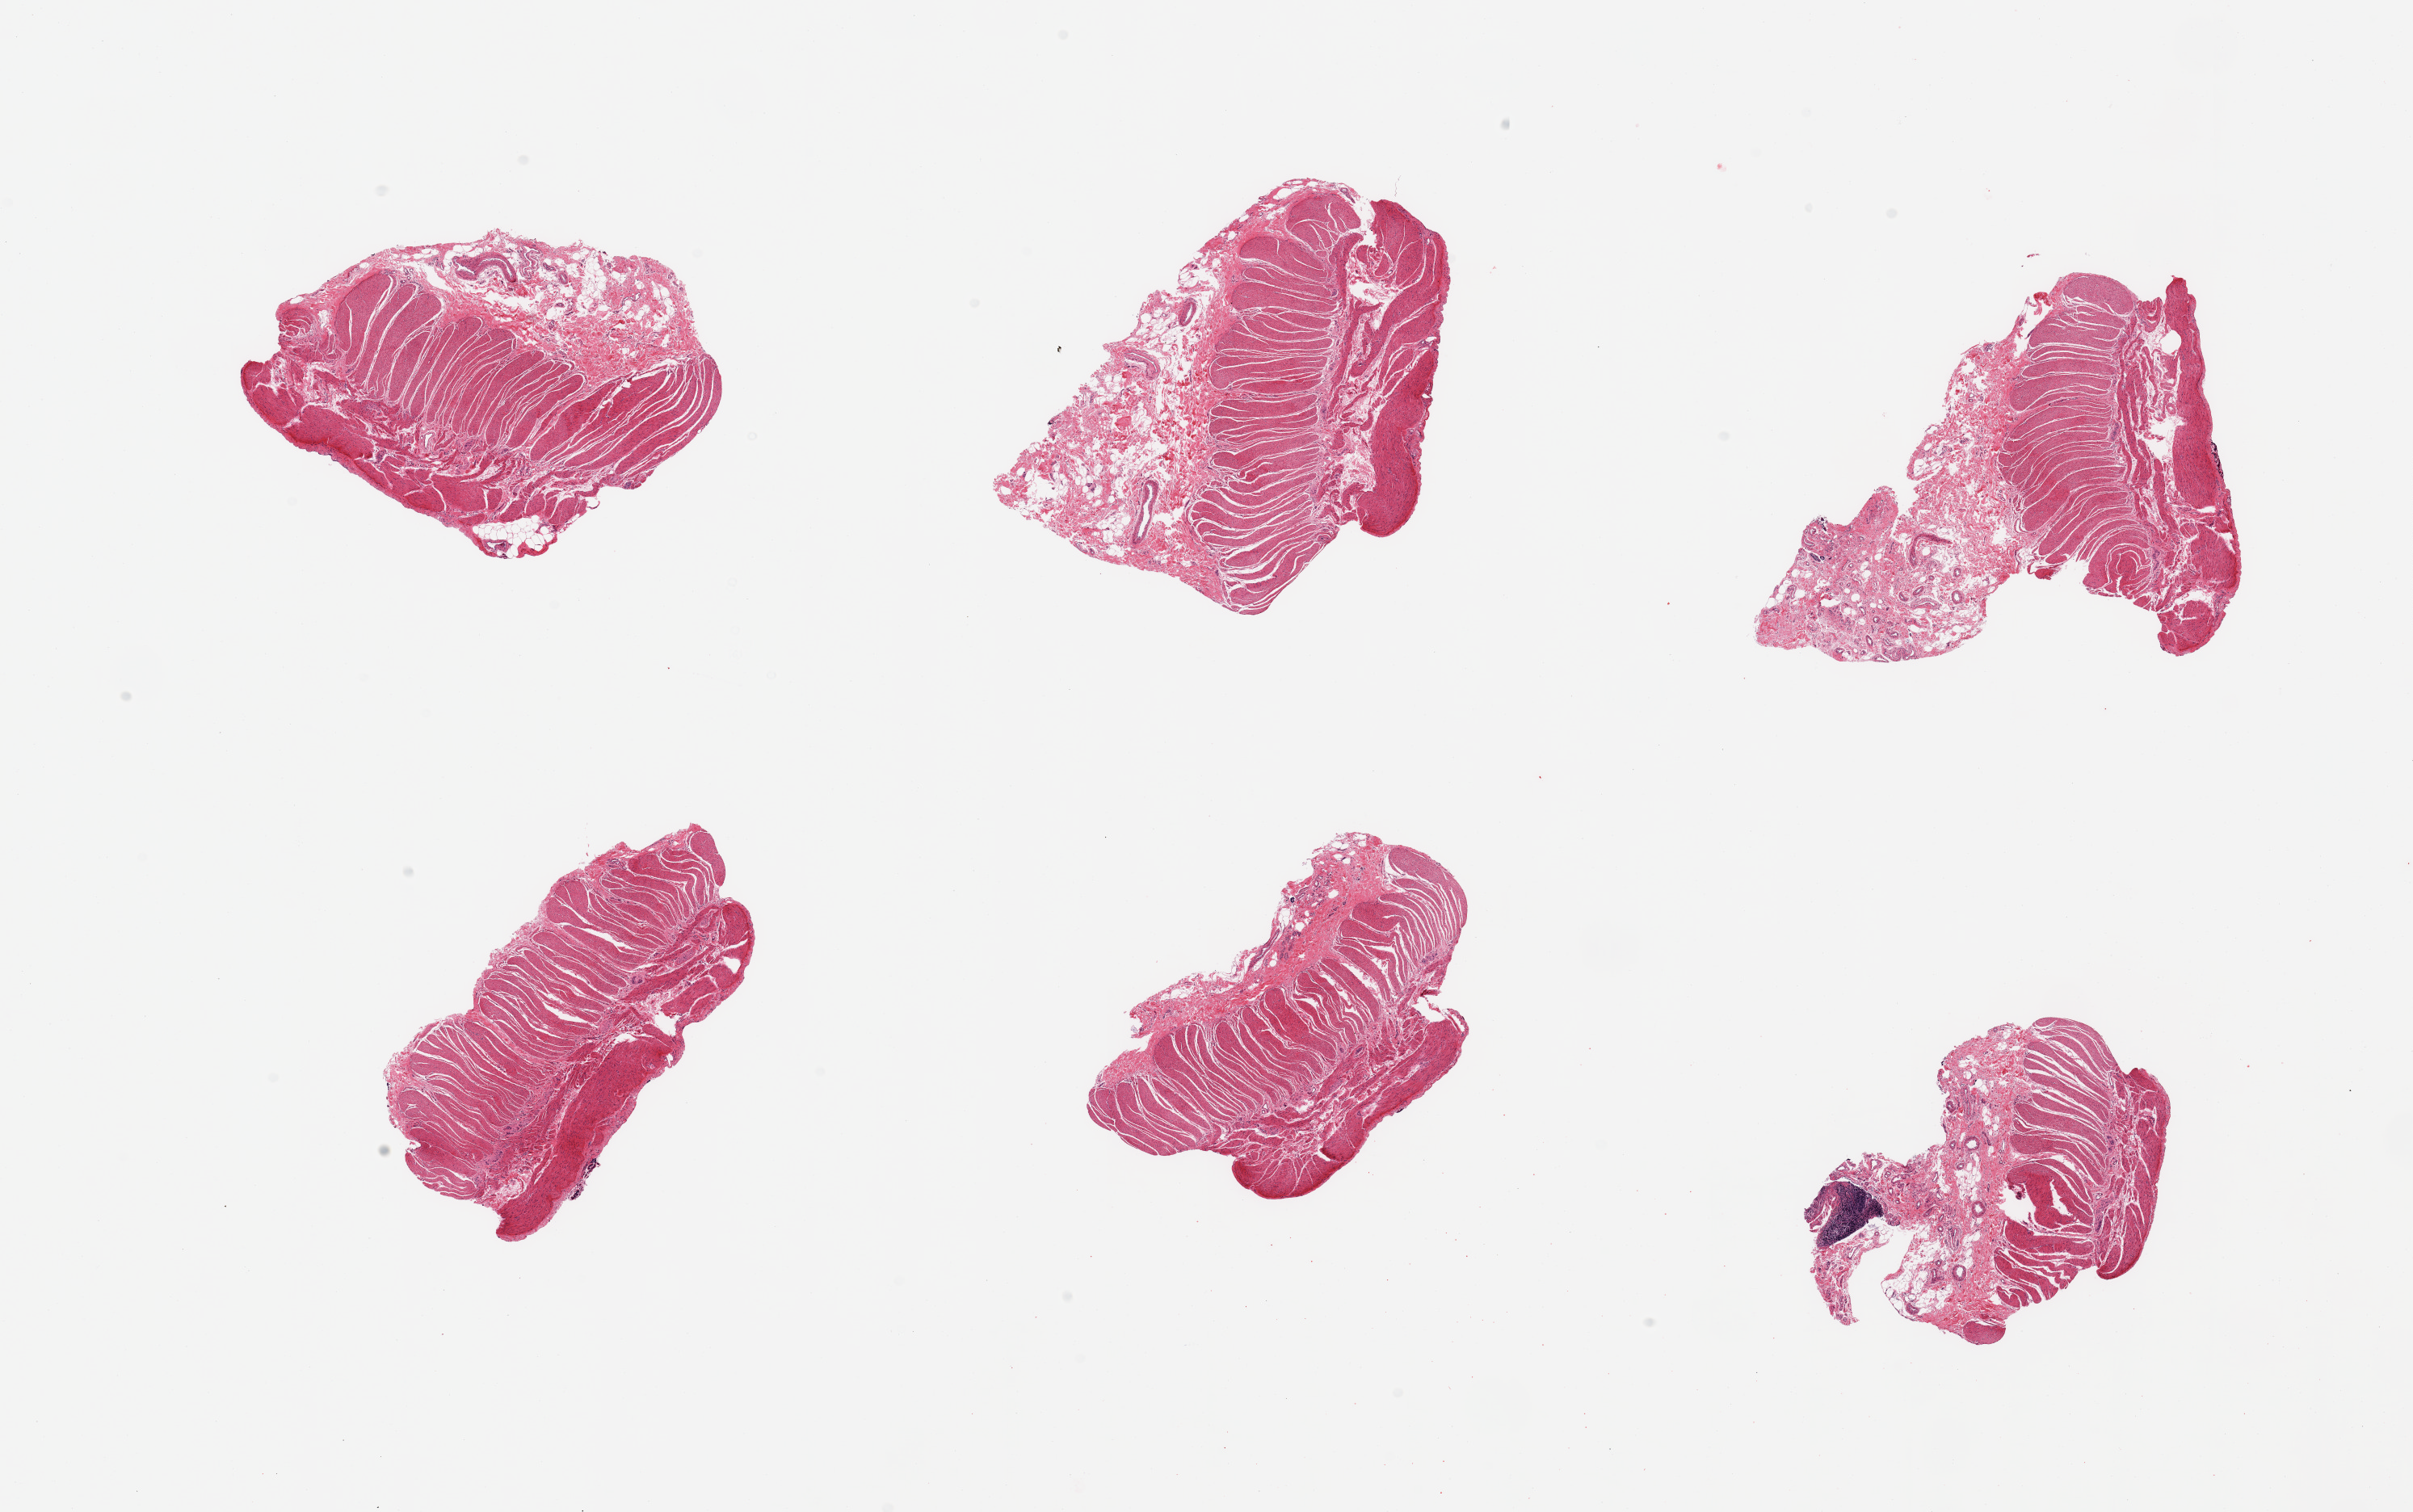
Hematoxylin and eosin (H&E) whole-slide image, shown as a low-resolution overview of the whole scanned area (about 23.6 x 14.8 mm), PAXgene-fixed paraffin-embedded (PFPE) section, section of sigmoid colon (target tissue), donor tissue sample. Male donor.
• pathologist's review note for this sample: 6 pieces, target muscularis, adherent fibroadipose tissue on most sections, 1-2mm nubbins